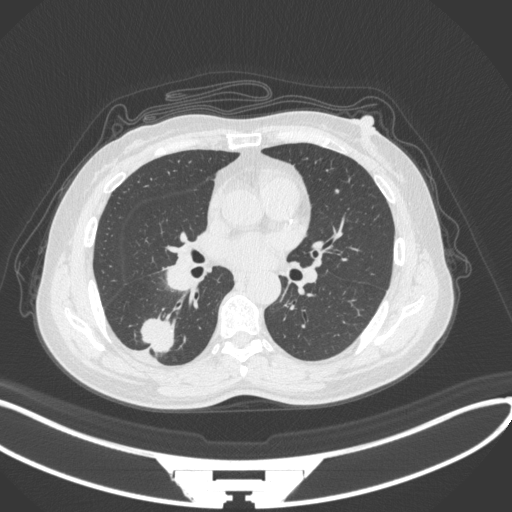
Chest CT, one axial slice. Position 153 of 352 along the scan axis. 120 kVp. Lung window (W 1500 / L -600 HU). 1 mm slice thickness. 512 × 512 image matrix. Patient: female, 55 years. From the clinical record (not read from this slice): clinical TNM (as recorded): T1c N1 M0.
Outlined on this slice (bounding box drawn by a radiologist):
- lung tumour (recorded histology: adenocarcinoma): bounding box [x1, y1, x2, y2] px = [140, 313, 179, 357]